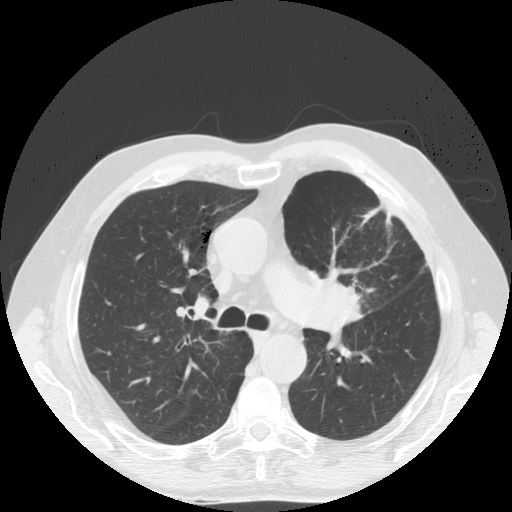
Low-dose screening chest CT, one axial slice. Position 114 of 170 along the scan axis. Reconstruction kernel STANDARD. Lung window (W 1500 / L -600 HU). 2.5 mm slice thickness. 512 × 512 image matrix, field of view 380 × 380 mm.
Annotated regions visible in this slice (outlined manually by an expert reader):
- lesion 1 (tumor, upper lobe of left lung): box from (x=314, y=279) to (x=363, y=322) px